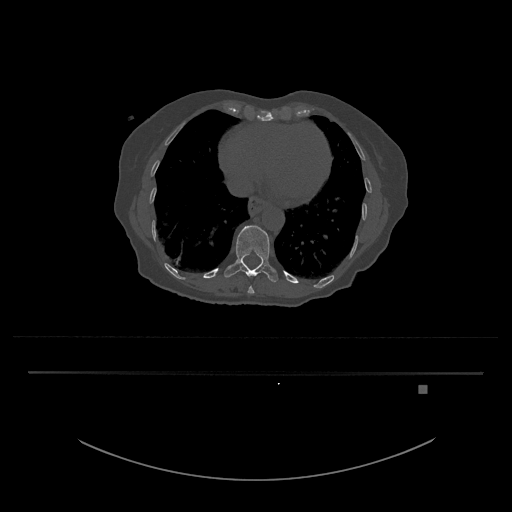
CT including the spine, one axial slice. Reconstruction kernel Br40s/3. Bone window (W 1800 / L 400 HU). 0.5 mm slice thickness. 512 × 512 image matrix, field of view 500 × 500 mm. Patient: female, 57 years. From the clinical record (not read from this slice): primary cancer: cervical.
Structures marked on this image (semi-automatic segmentation, software-assisted and operator-edited):
- T10 vertebra: bounding box <248,287,255,294> (left, top, right, bottom; pixels)
- T11 vertebra: <224,225,278,282>